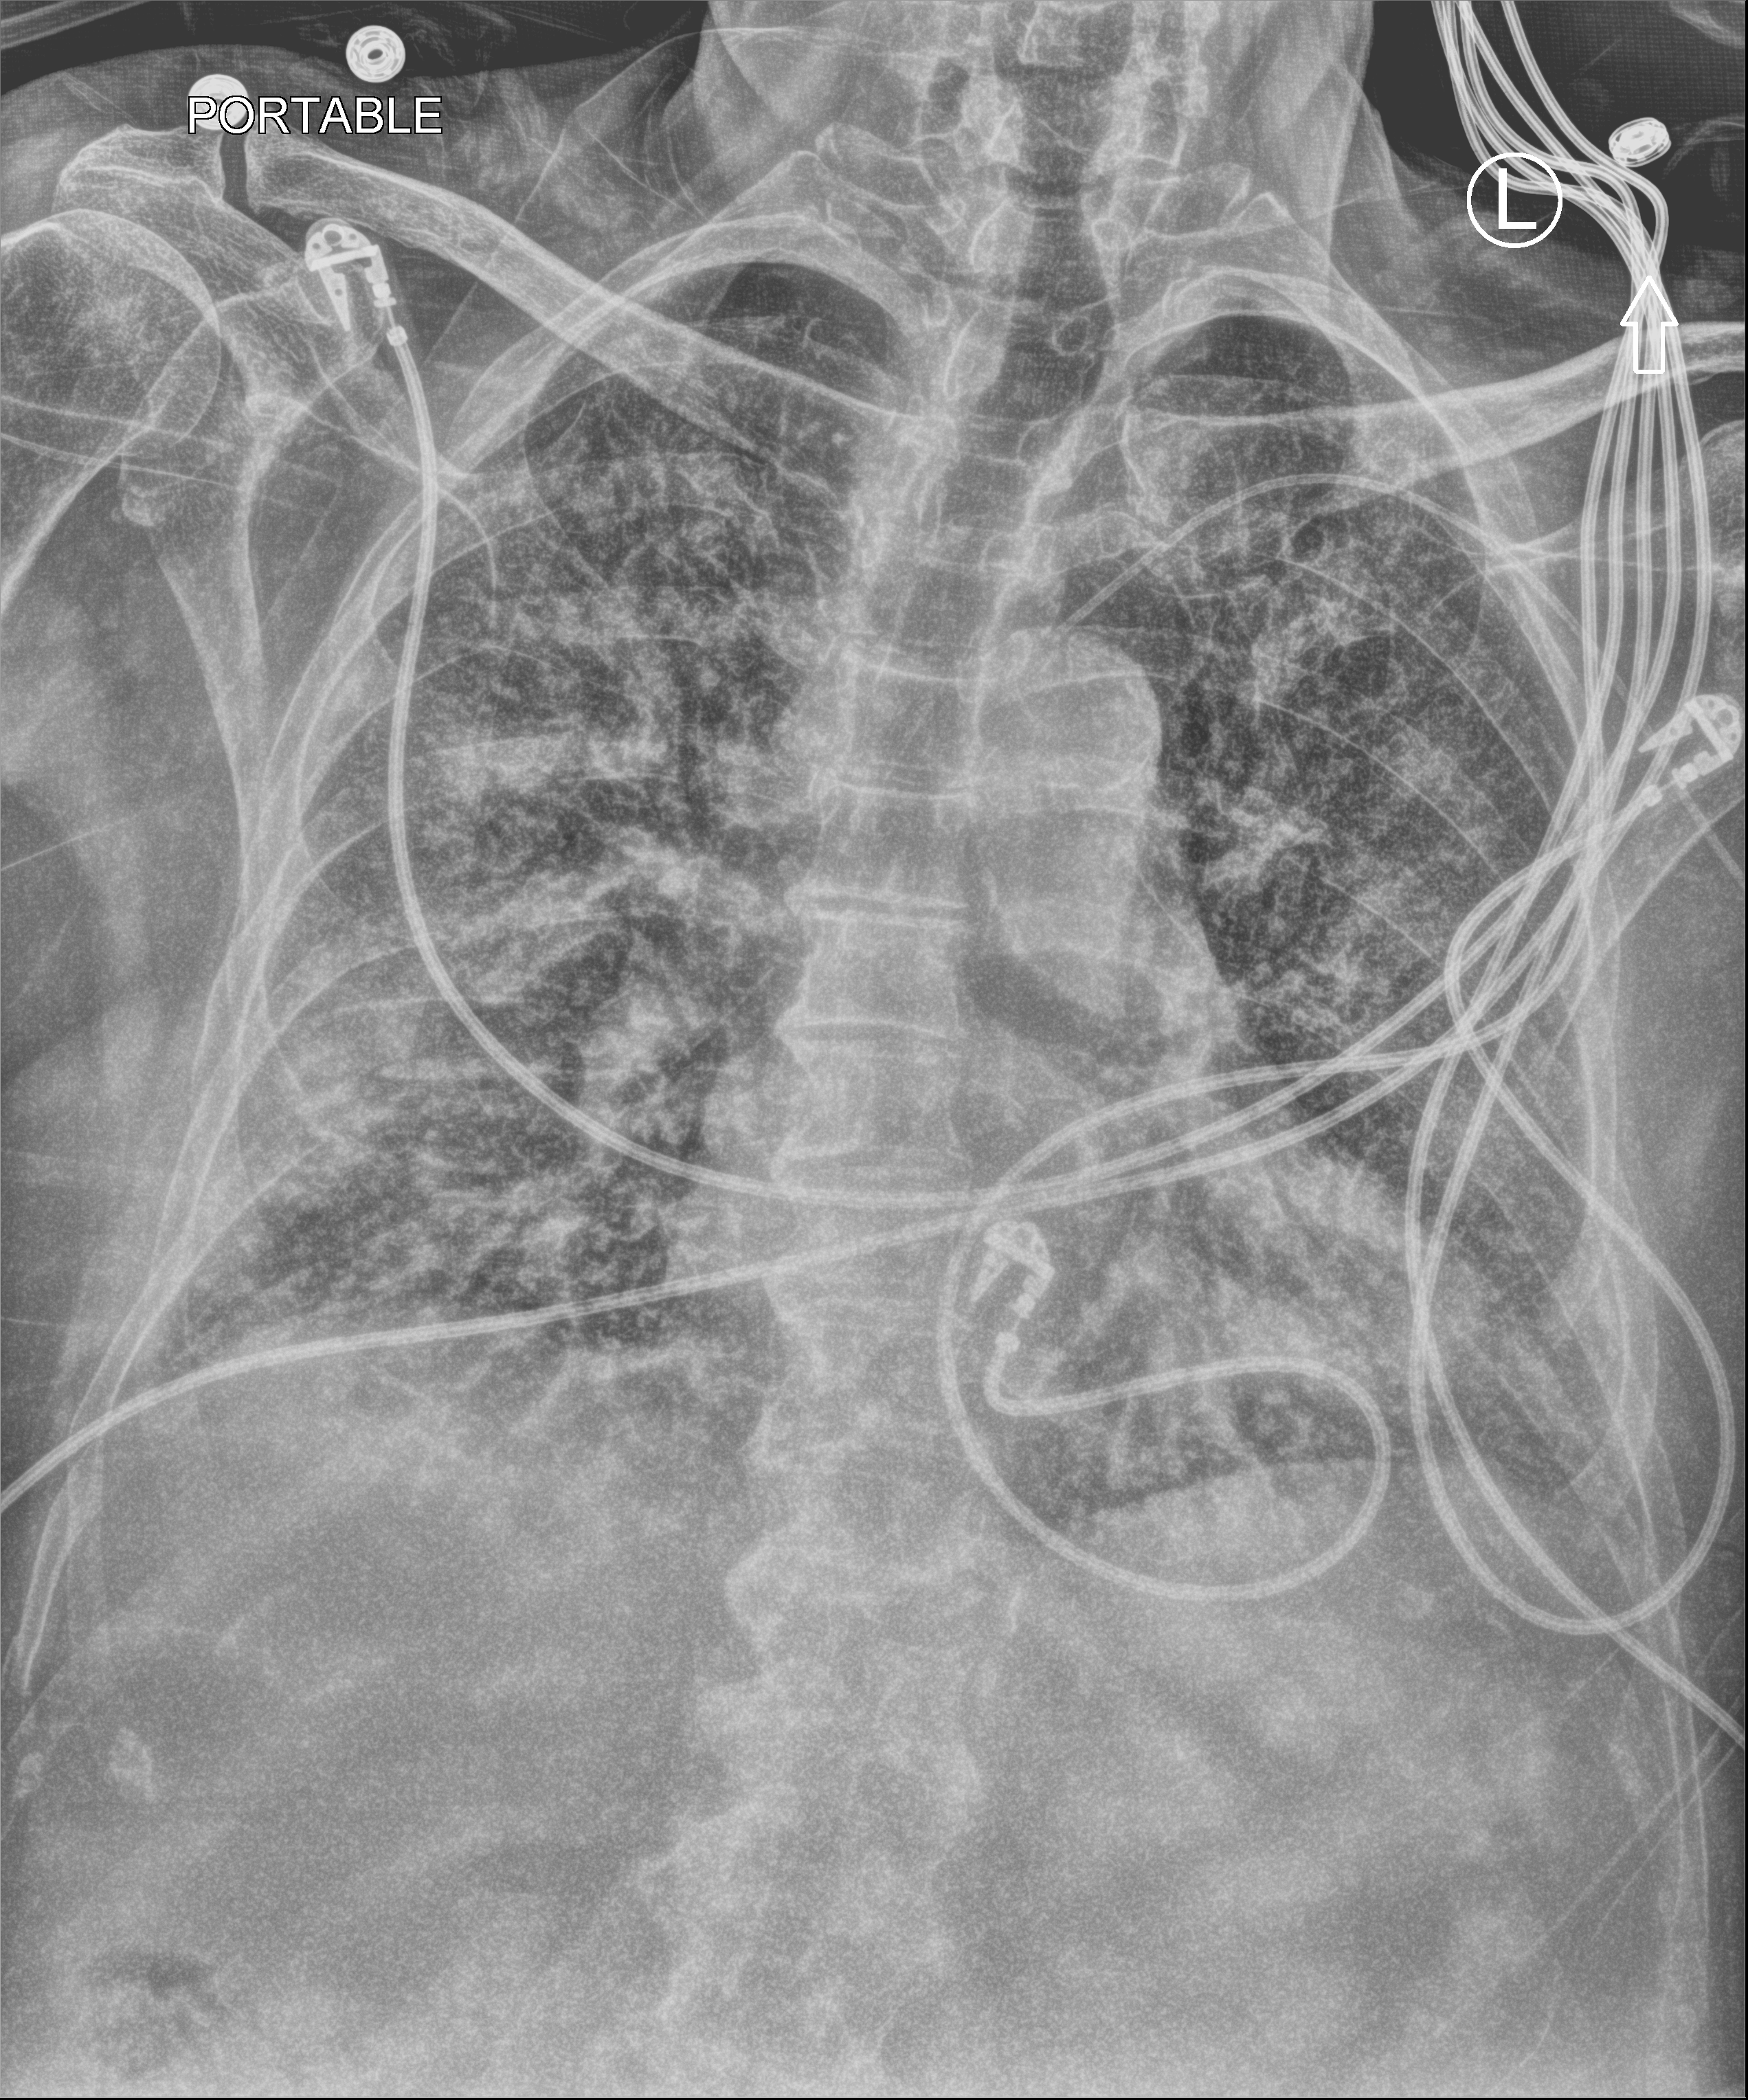
Chest X-ray (portable). Male patient hospitalised with COVID-19, age 75–90 years.
Admission-level facts for this patient (not findings on this image; timing relative to this image not recorded):
- other chronic lung disease (admission record): no
- mechanically ventilated during this hospital stay: yes
- admitted to intensive care during this hospital stay: yes